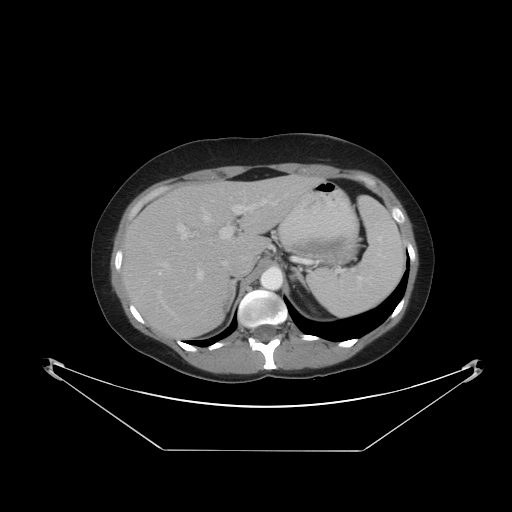
Contrast-enhanced abdominal CT, one axial slice. Slice 31 of 48 in the series (ordered by position). Reconstruction kernel STANDARD. 120 kVp. Intravenous contrast given. Soft-tissue window (W 400 / L 40 HU). 512 × 512 image matrix. Female patient, age 38 years. From the clinical record (not read from this slice): diagnosis: colorectal cancer liver metastases, imaged before liver resection; multiple liver metastases: yes; largest metastasis: 2.5 cm; chemotherapy before resection: no.
Outlined on this slice (outlined manually by an expert reader):
- hepatic veins: bounding box [x1, y1, x2, y2] px = [158, 190, 247, 293]
- liver: [120, 175, 319, 340]
- planned liver remnant (the part of the liver to remain after resection): [171, 176, 305, 256]
- portal vein (with intrahepatic branches): [177, 195, 278, 281]